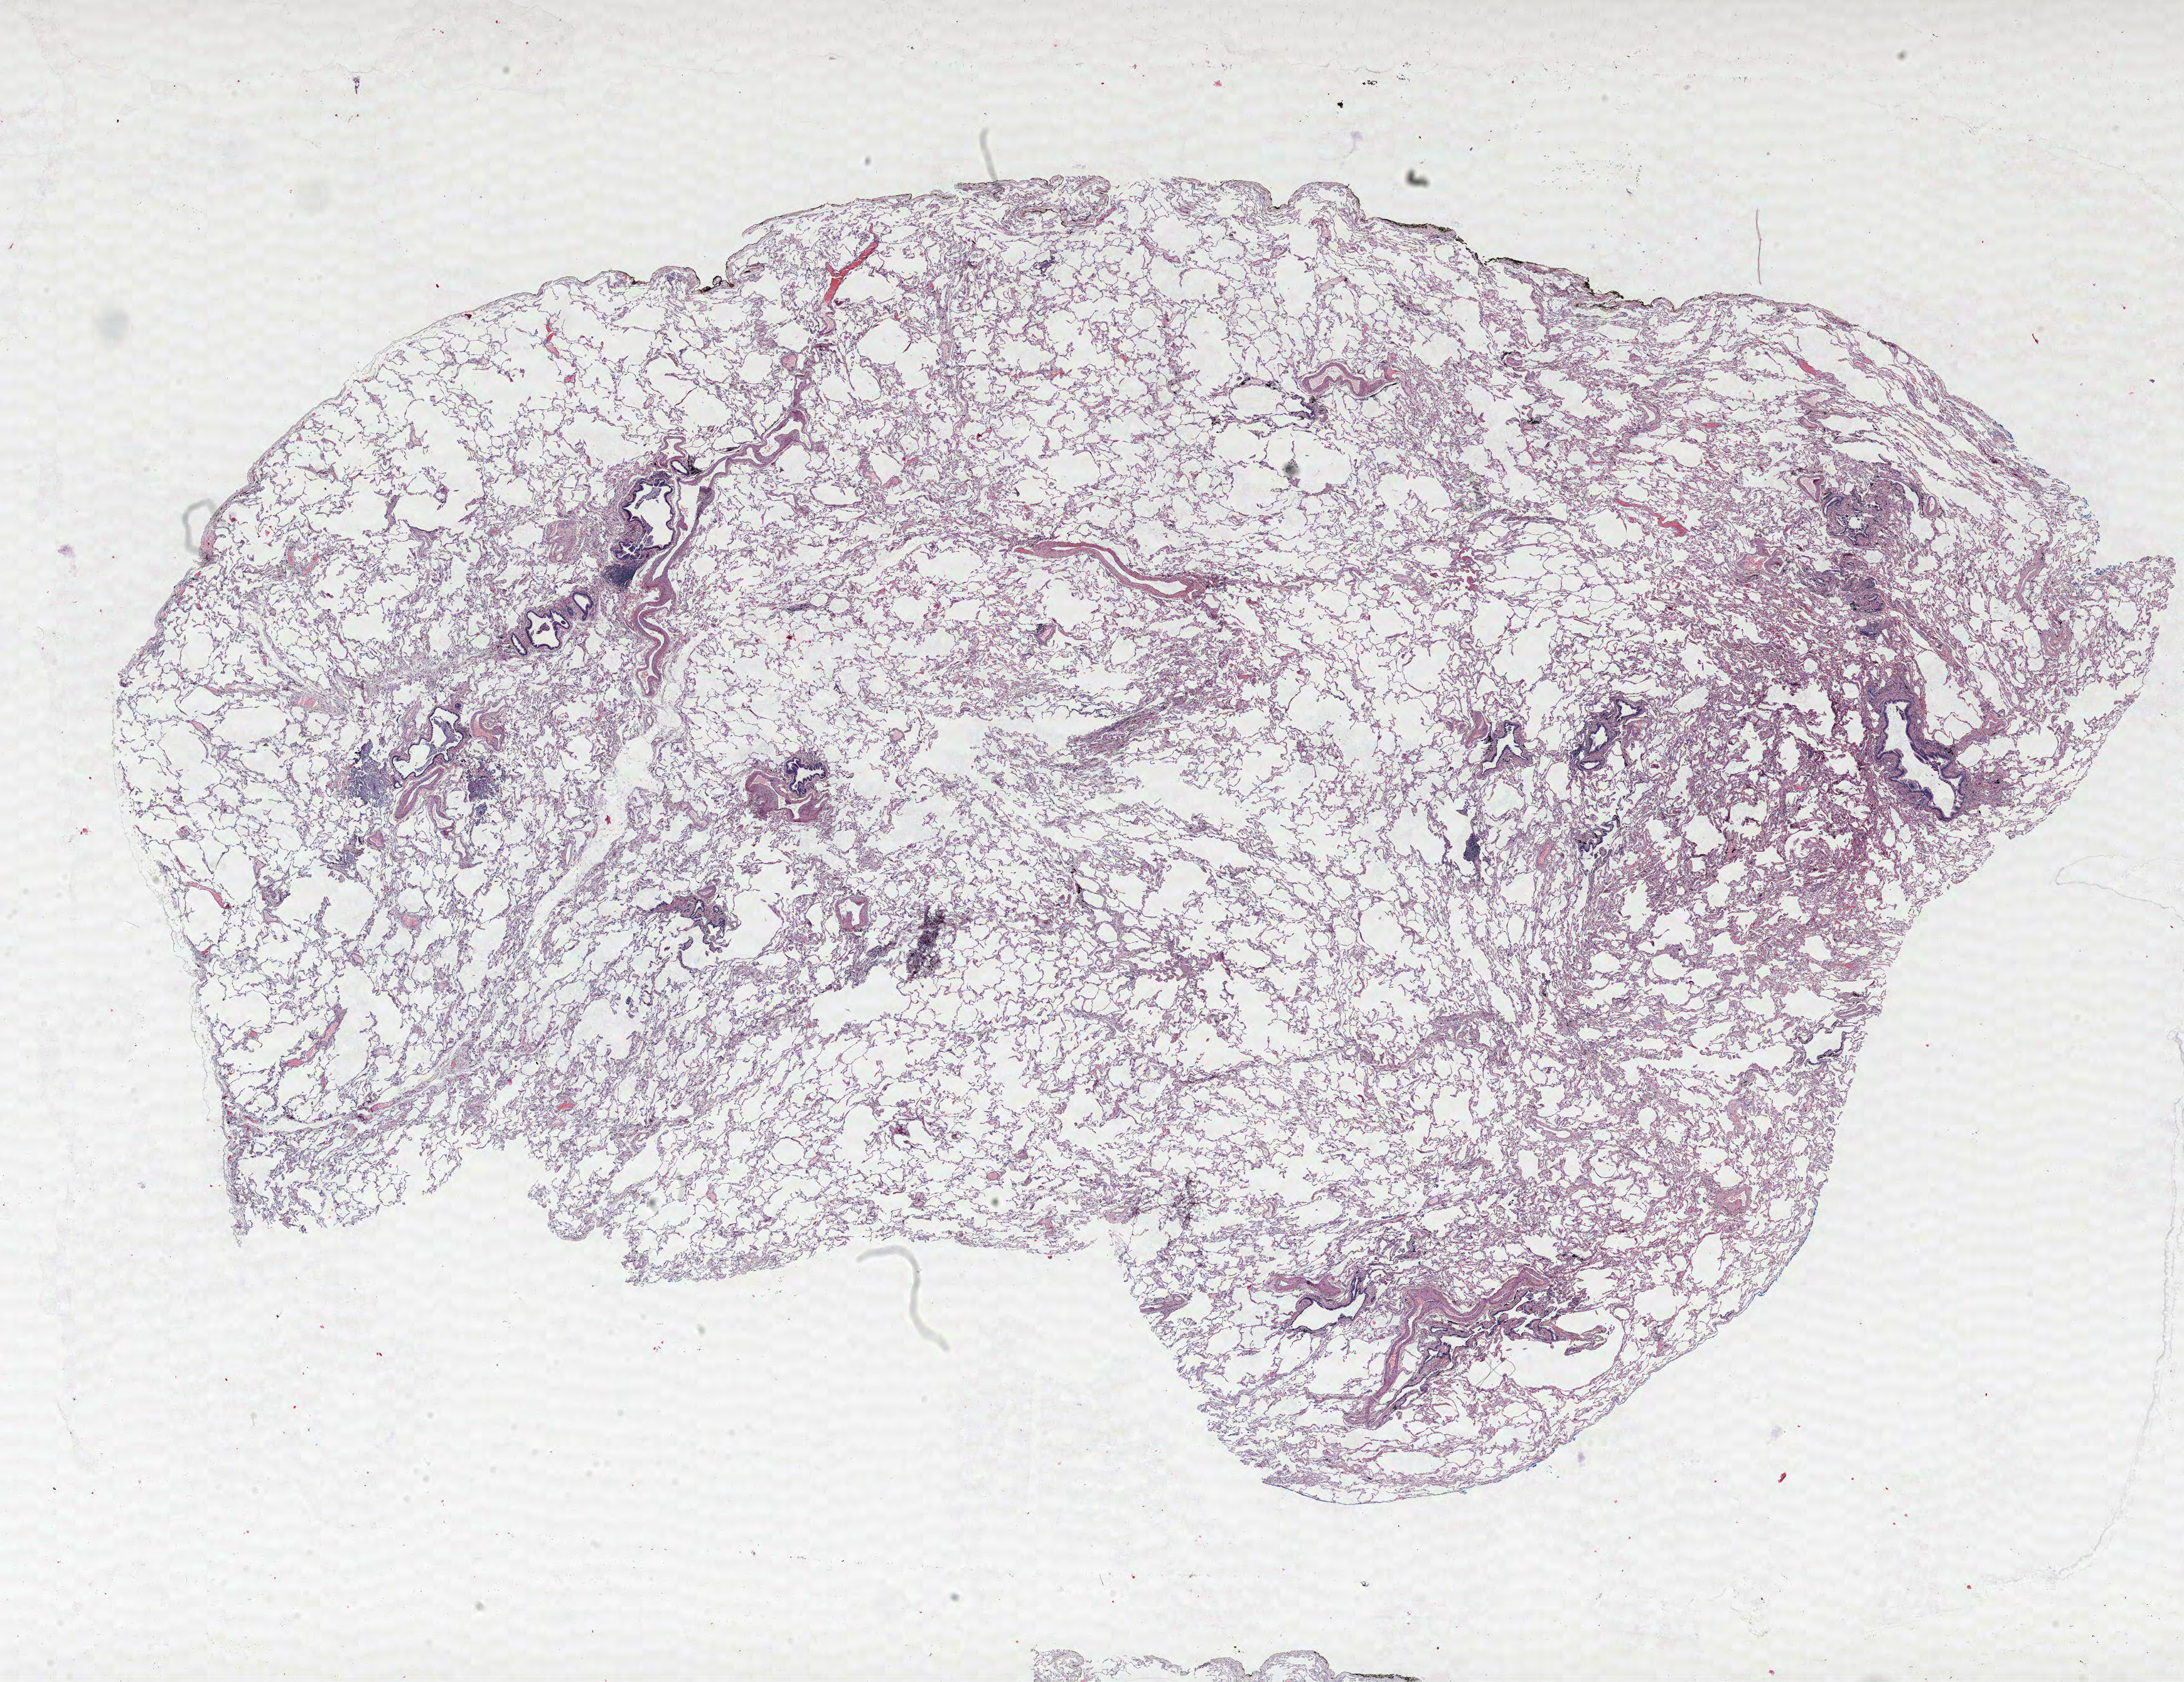
H&E whole-slide image — whole scanned area (about 27.8 x 21.4 mm, acquisition: 40x scan) shown as a low-resolution overview; formalin-fixed paraffin-embedded (FFPE) section; lung tissue. Female patient, aged 72 at enrolment. Current smoker at enrolment. Grade: well differentiated (G1).
- tumour size (pathology): 23 mm
- ICD-O-3 topography: upper lobe of lung (C34.1)
- participant's lung-cancer diagnosis: Bronchiolo-alveolar adenocarcinoma, NOS
- stage (AJCC 6th edition): IA
- primary tumour location (clinical record): right upper lobe